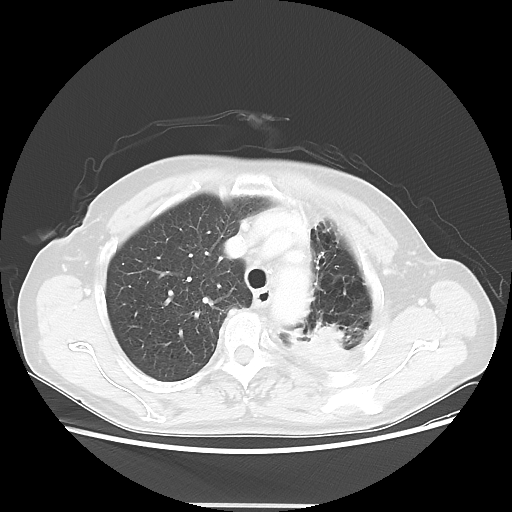
Chest CT, one axial slice; position 41 of 56 along the scan axis; reconstruction kernel LUNG; 100 kVp; lung window (W 1500 / L -600 HU); 5 mm slice thickness; 512 × 512 image matrix, field of view 377 × 377 mm. Patient: female, 63 years. From the clinical record (not read from this slice): clinical TNM (as recorded): T2a N0 M0.
Outlined on this slice (rectangle marked by the reading radiologist):
- lung tumour (recorded histology: adenocarcinoma): bounding box [x1, y1, x2, y2] px = [301, 323, 353, 364]